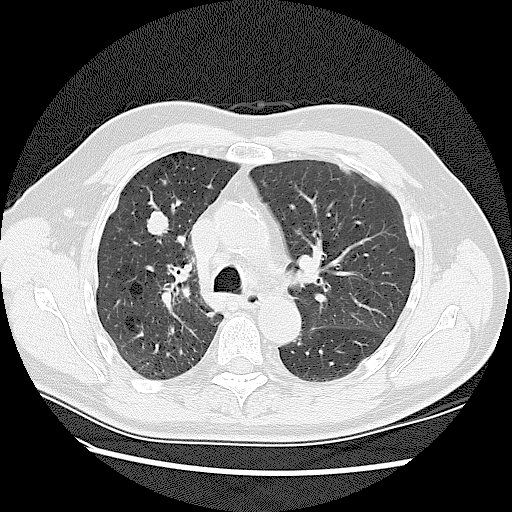
Axial slice from a low-dose chest CT screening exam, first (baseline) screen, lung window (W 1500 / L -600 HU), lung (sharp) reconstruction kernel (LUNG), slice 44 of 128 in the series, 512 × 512 image matrix. Male, age 72 years at enrolment.
Expert-annotated lung lesion, bounding box <133,202,182,240> (left, top, right, bottom; pixels). The screening reader recorded 2 non-calcified nodules or masses ≥4 mm on this exam (right upper lobe, right upper lobe); which of them this box marks is not recorded. Official screen result: positive, change unspecified: nodule(s) >= 4 mm or enlarging nodule(s), mass(es), or other non-specific abnormalities suspicious for lung cancer. Participant outcome: lung cancer diagnosed 42 days after this screen — adenocarcinoma, NOS, right upper lobe, stage IV (AJCC 6th edition), 45 mm at pathology.